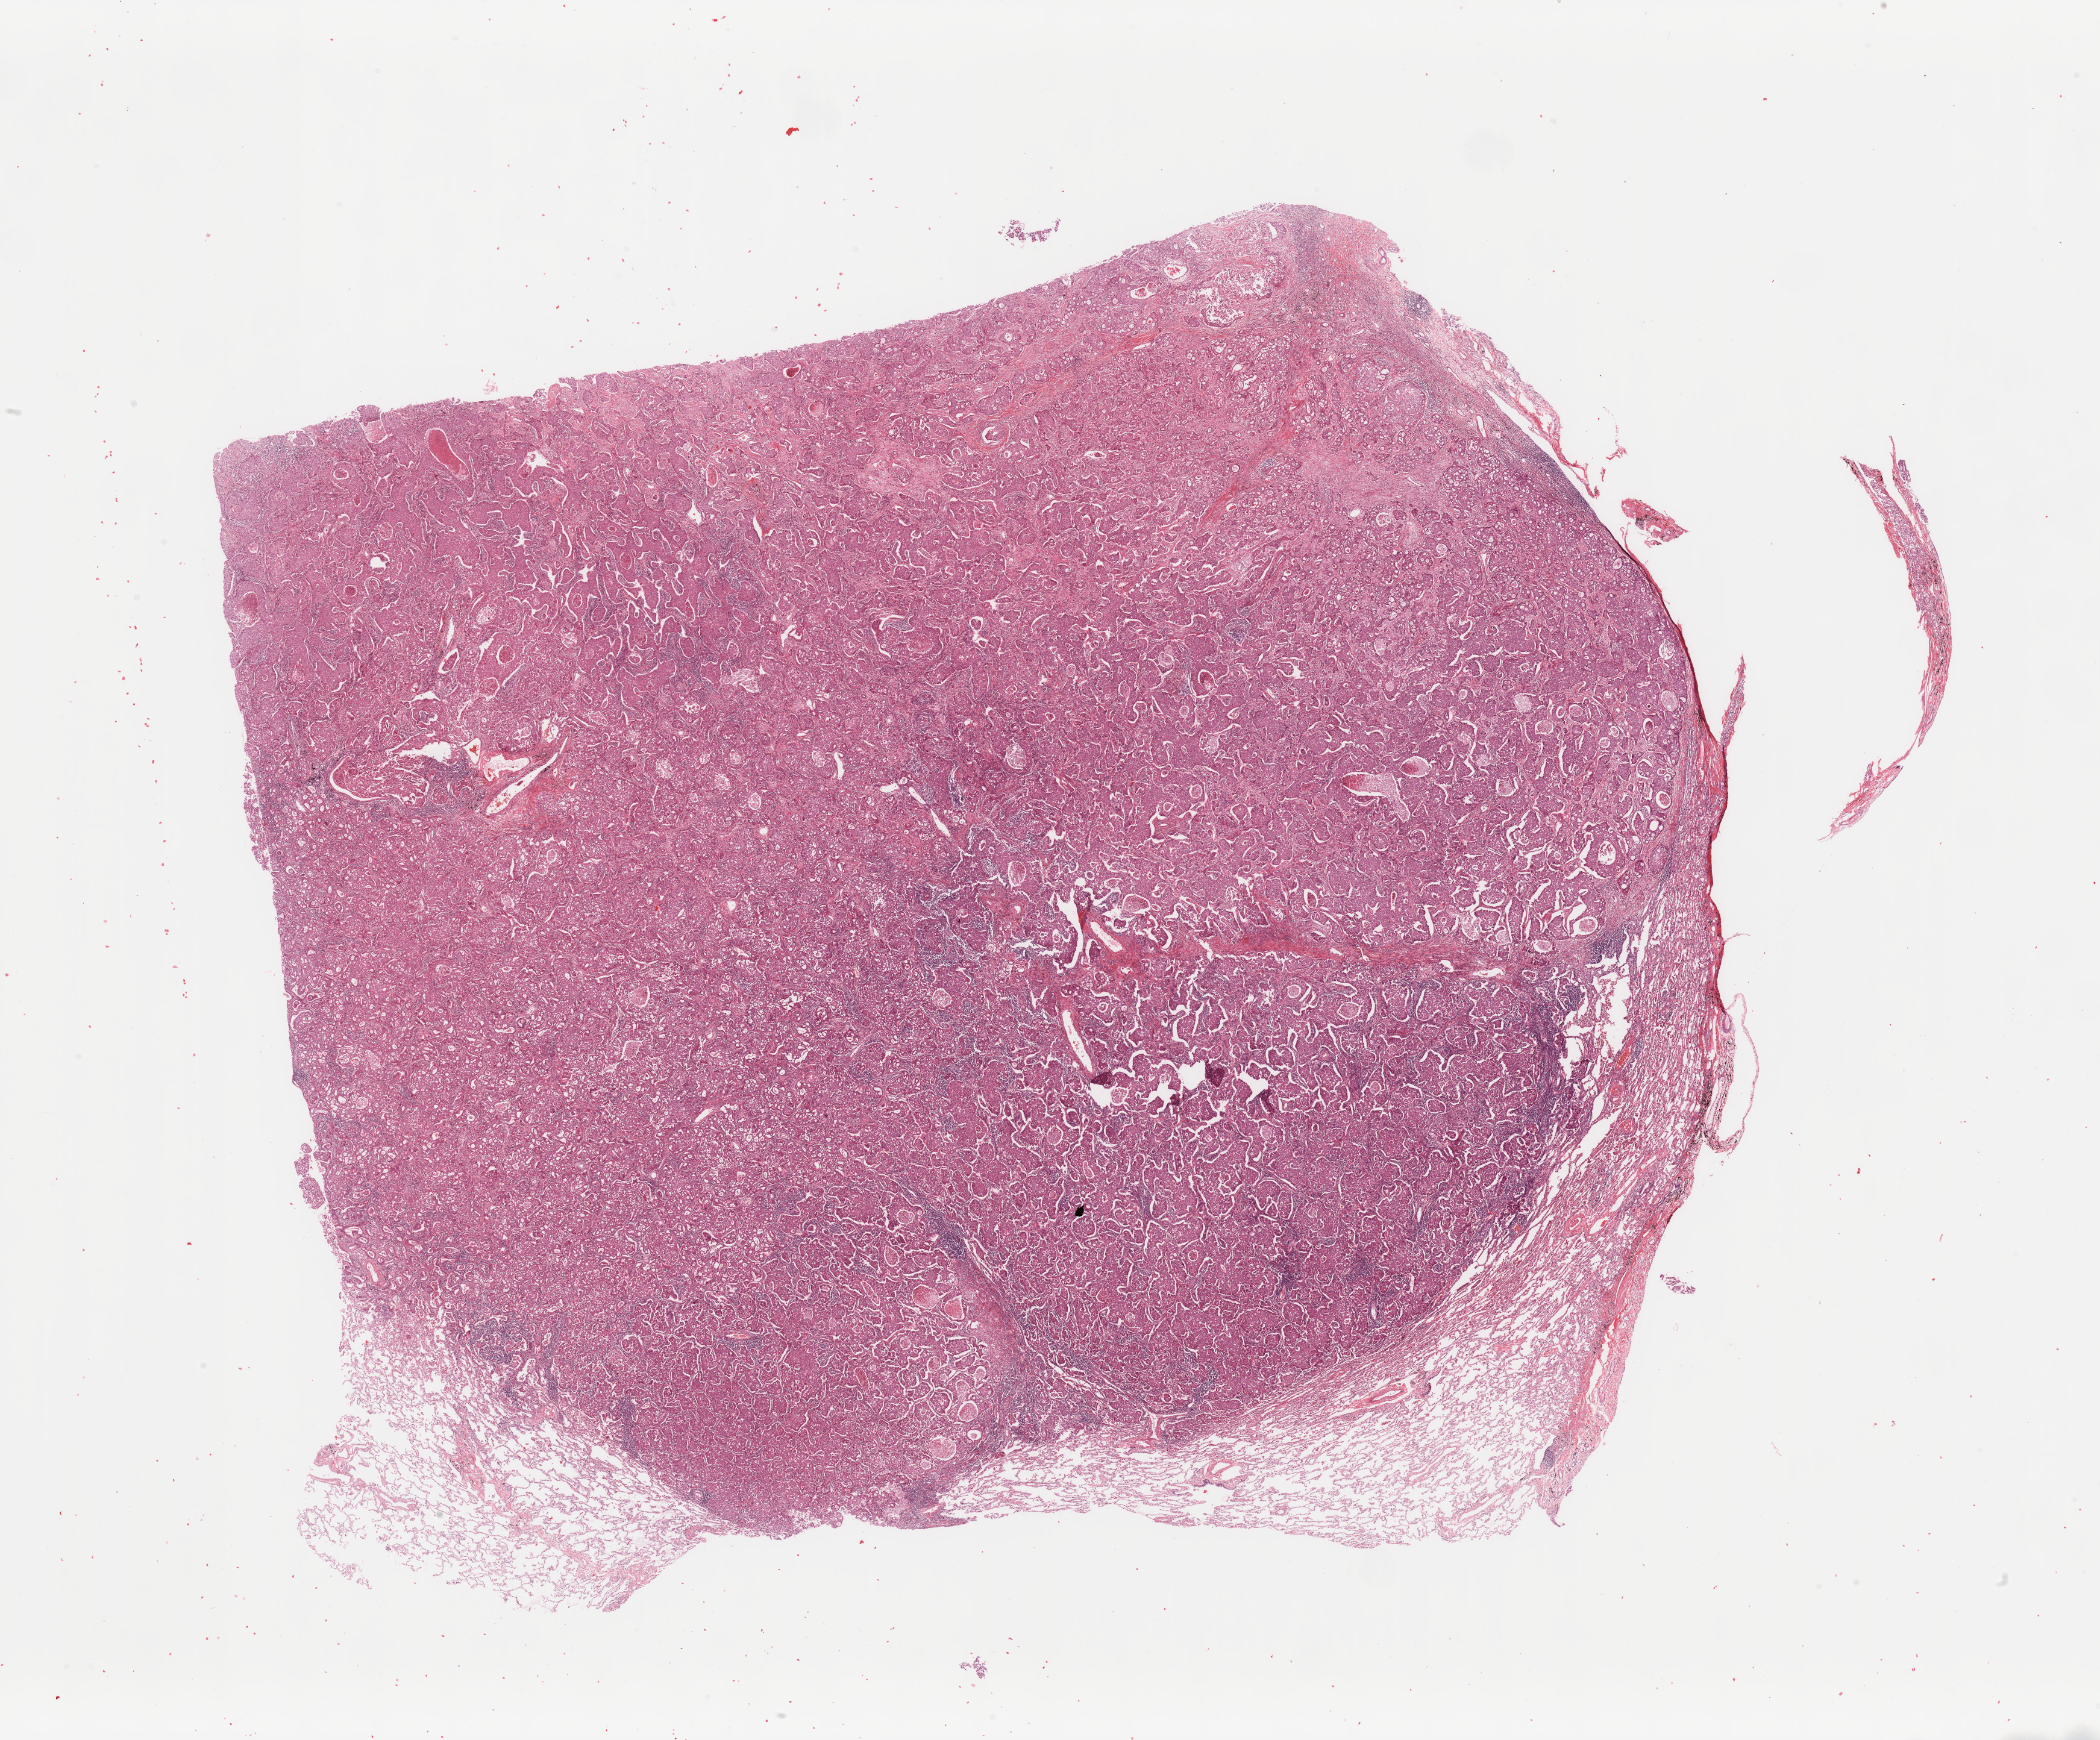
Digitized Hematoxylin and eosin (H&E) stained tissue section (whole slide), shown as a low-resolution overview of the whole scanned area (about 27.6 x 22.8 mm, from a 20x scan); tumour tissue sample, sampled site: lung. Female, 54 y/o. Histologic grade: G2 (moderately differentiated). Composition of this section per pathologist review: tumour nuclei 80%, necrosis 5%.
Histologic diagnosis: Adenocarcinoma, NOS. AJCC pathologic stage: IIIA.